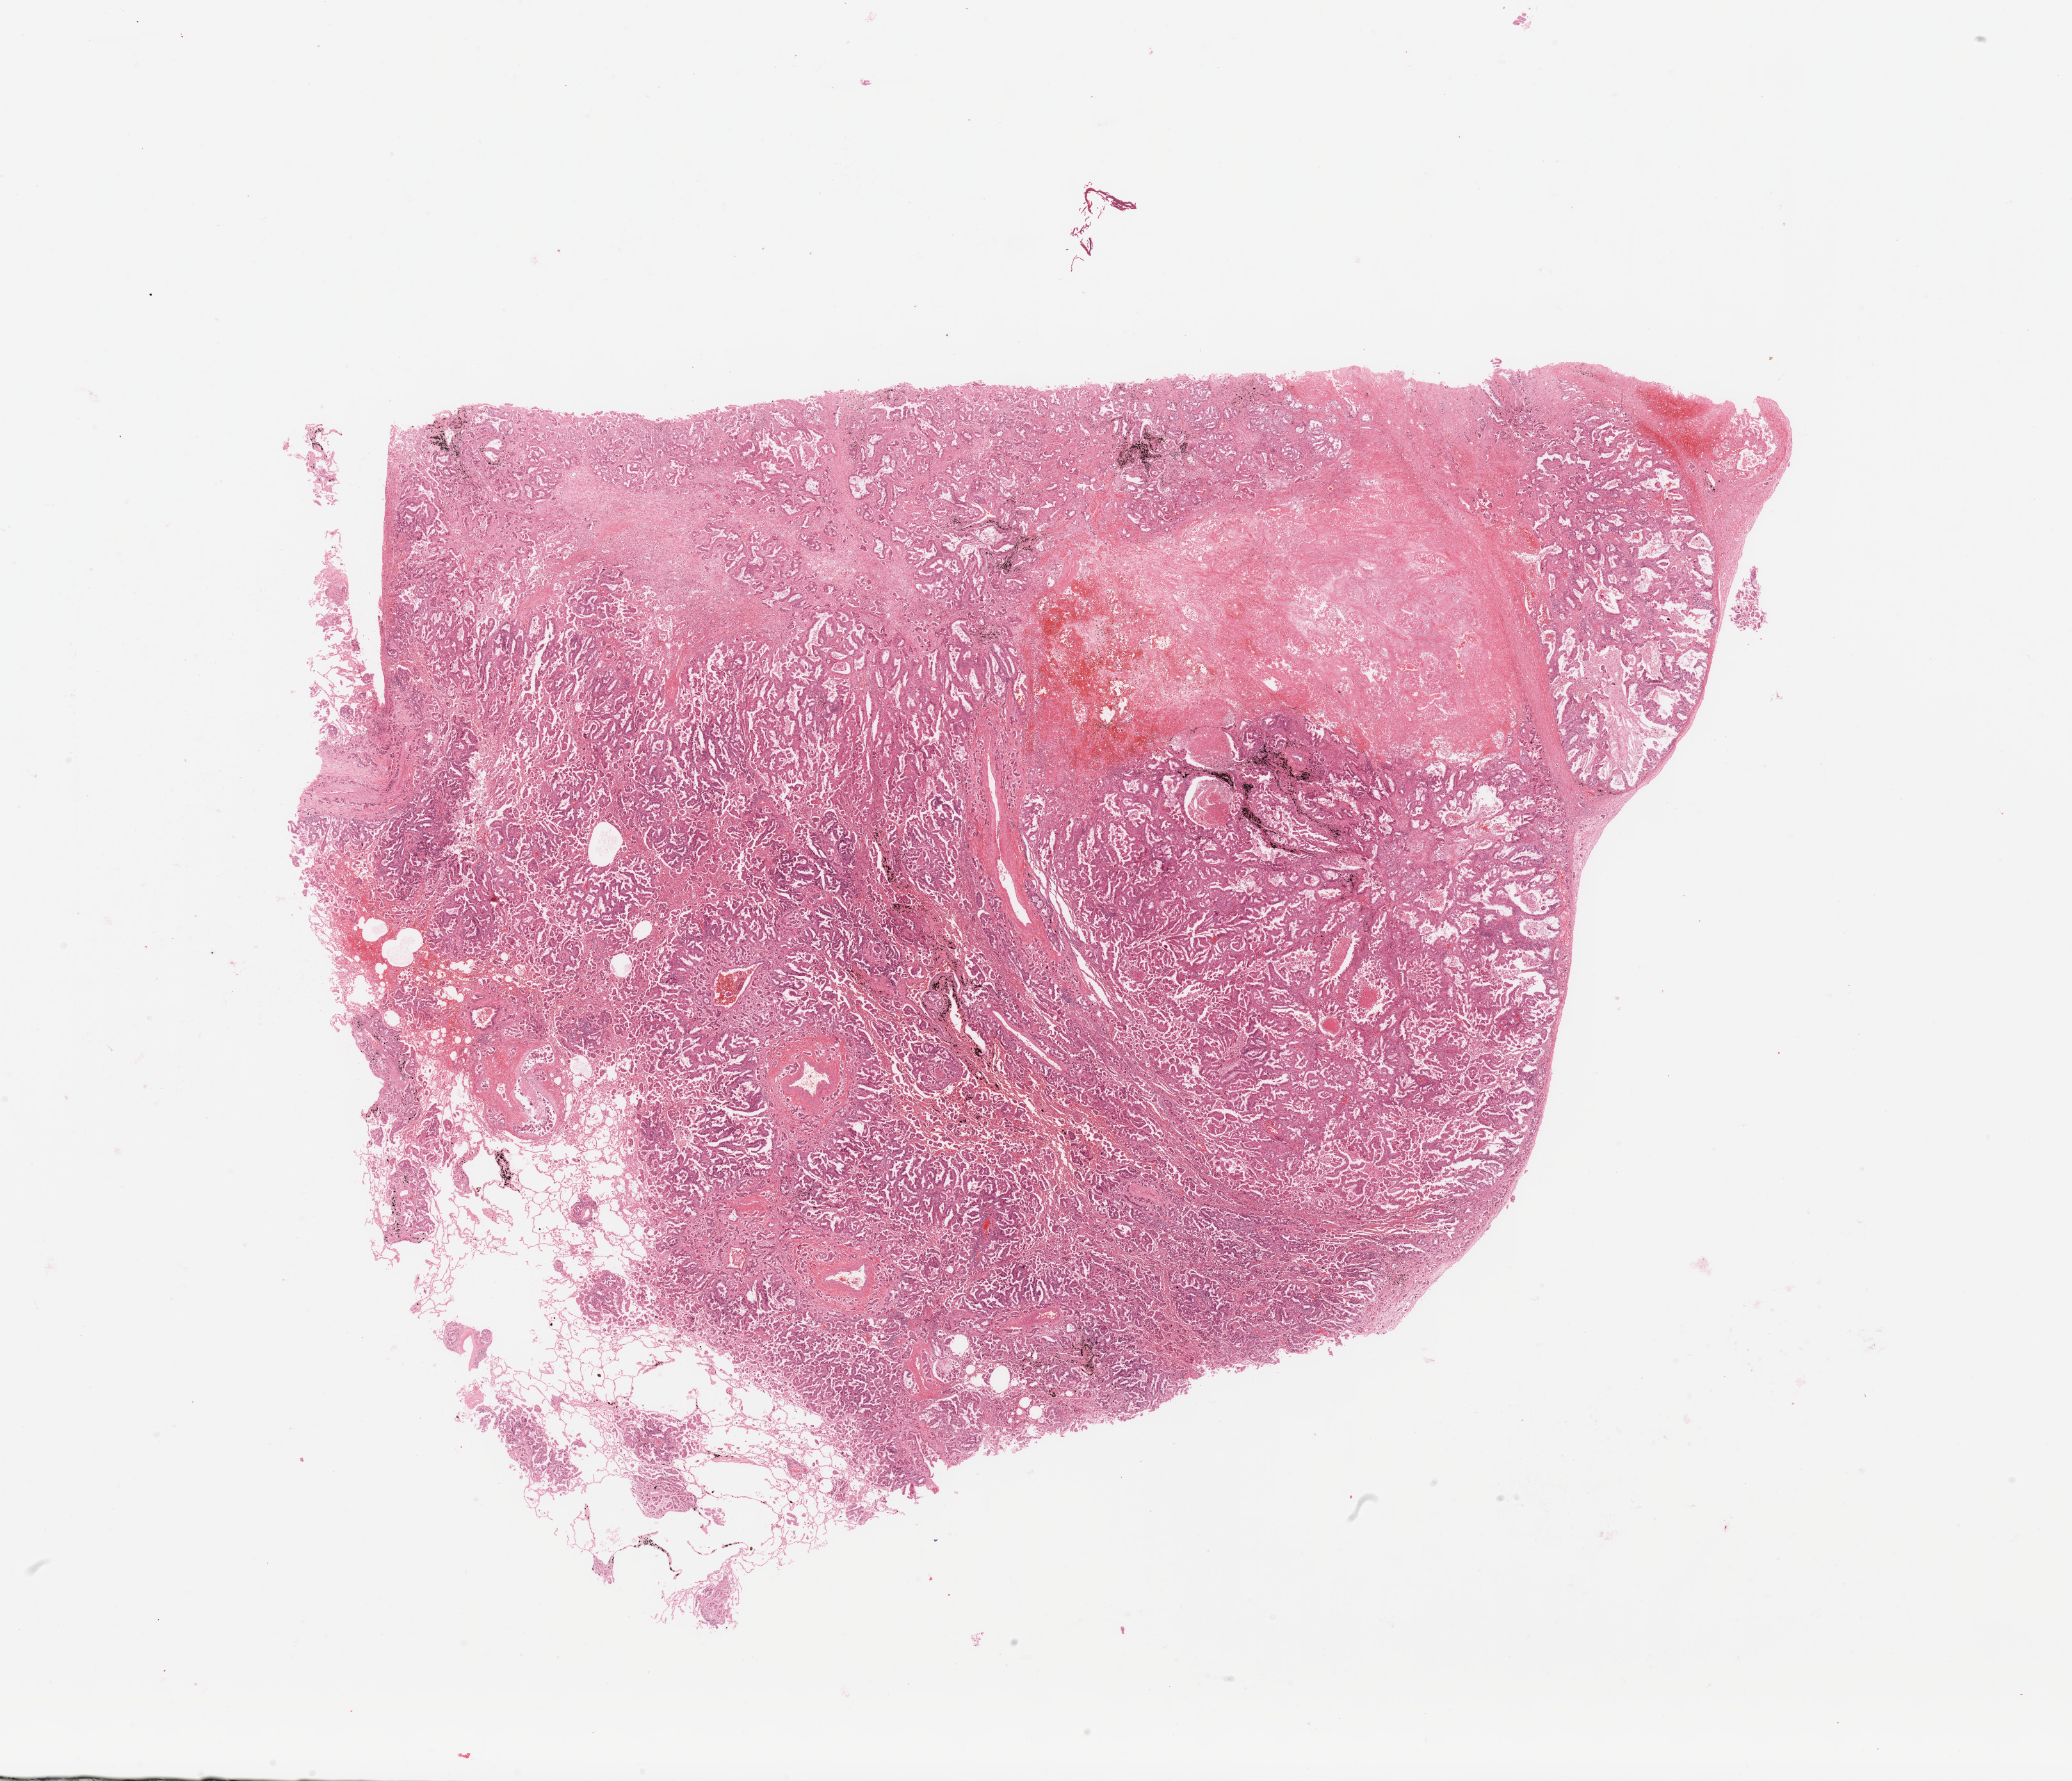
Digitized H&E tissue section (whole slide), whole scanned area (about 25.6 x 22.0 mm, from a 20x scan) shown as a low-resolution overview, tumour tissue sample, lung. Patient: male, age 64 years.
Diagnosis: Adenocarcinoma, NOS.